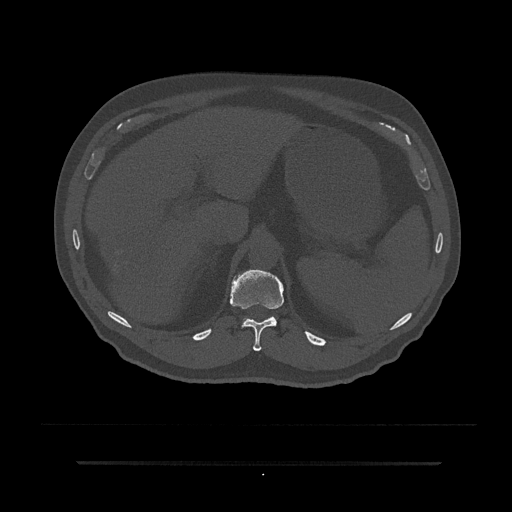
CT including the spine, one axial slice; slice 254 of 797 in the series (ordered by position); reconstruction kernel Br40s/3; 120 kVp; bone window (W 1800 / L 400 HU); 0.5 mm slice thickness; 512 × 512 image matrix, field of view 464 × 464 mm. Patient: male, 59 years. Case-level facts recorded for this patient, not image findings: primary cancer: bile ducts; vertebrae with lytic lesions (as recorded): T10.
Annotated regions visible in this slice (semi-automatic segmentation, software-assisted and operator-edited):
- T11 vertebra: bounding box (x1, y1, x2, y2) in pixels: (230, 269, 284, 352)
- T12 vertebra: (243, 316, 276, 324)